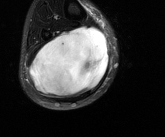
MRI of an extremity soft-tissue mass, one axial slice. Slice 54 of 81 in the series (ordered by position). T2-weighted fat-saturated. MR volume resampled by the dataset authors to the PET/CT grid (not the native acquisition matrix). 3.27 mm slice thickness. 165 × 137 image matrix, field of view 161 × 134 mm. Male patient. From the clinical record (not read from this slice): histological type: liposarcoma - round cell; grade: high; site of the primary tumour: right calf.
Annotated regions visible in this slice (expert contour drawn on MRI and transferred to this co-registered scan by the dataset authors):
- gross tumour volume (mass): box from (x=30, y=27) to (x=108, y=99) px